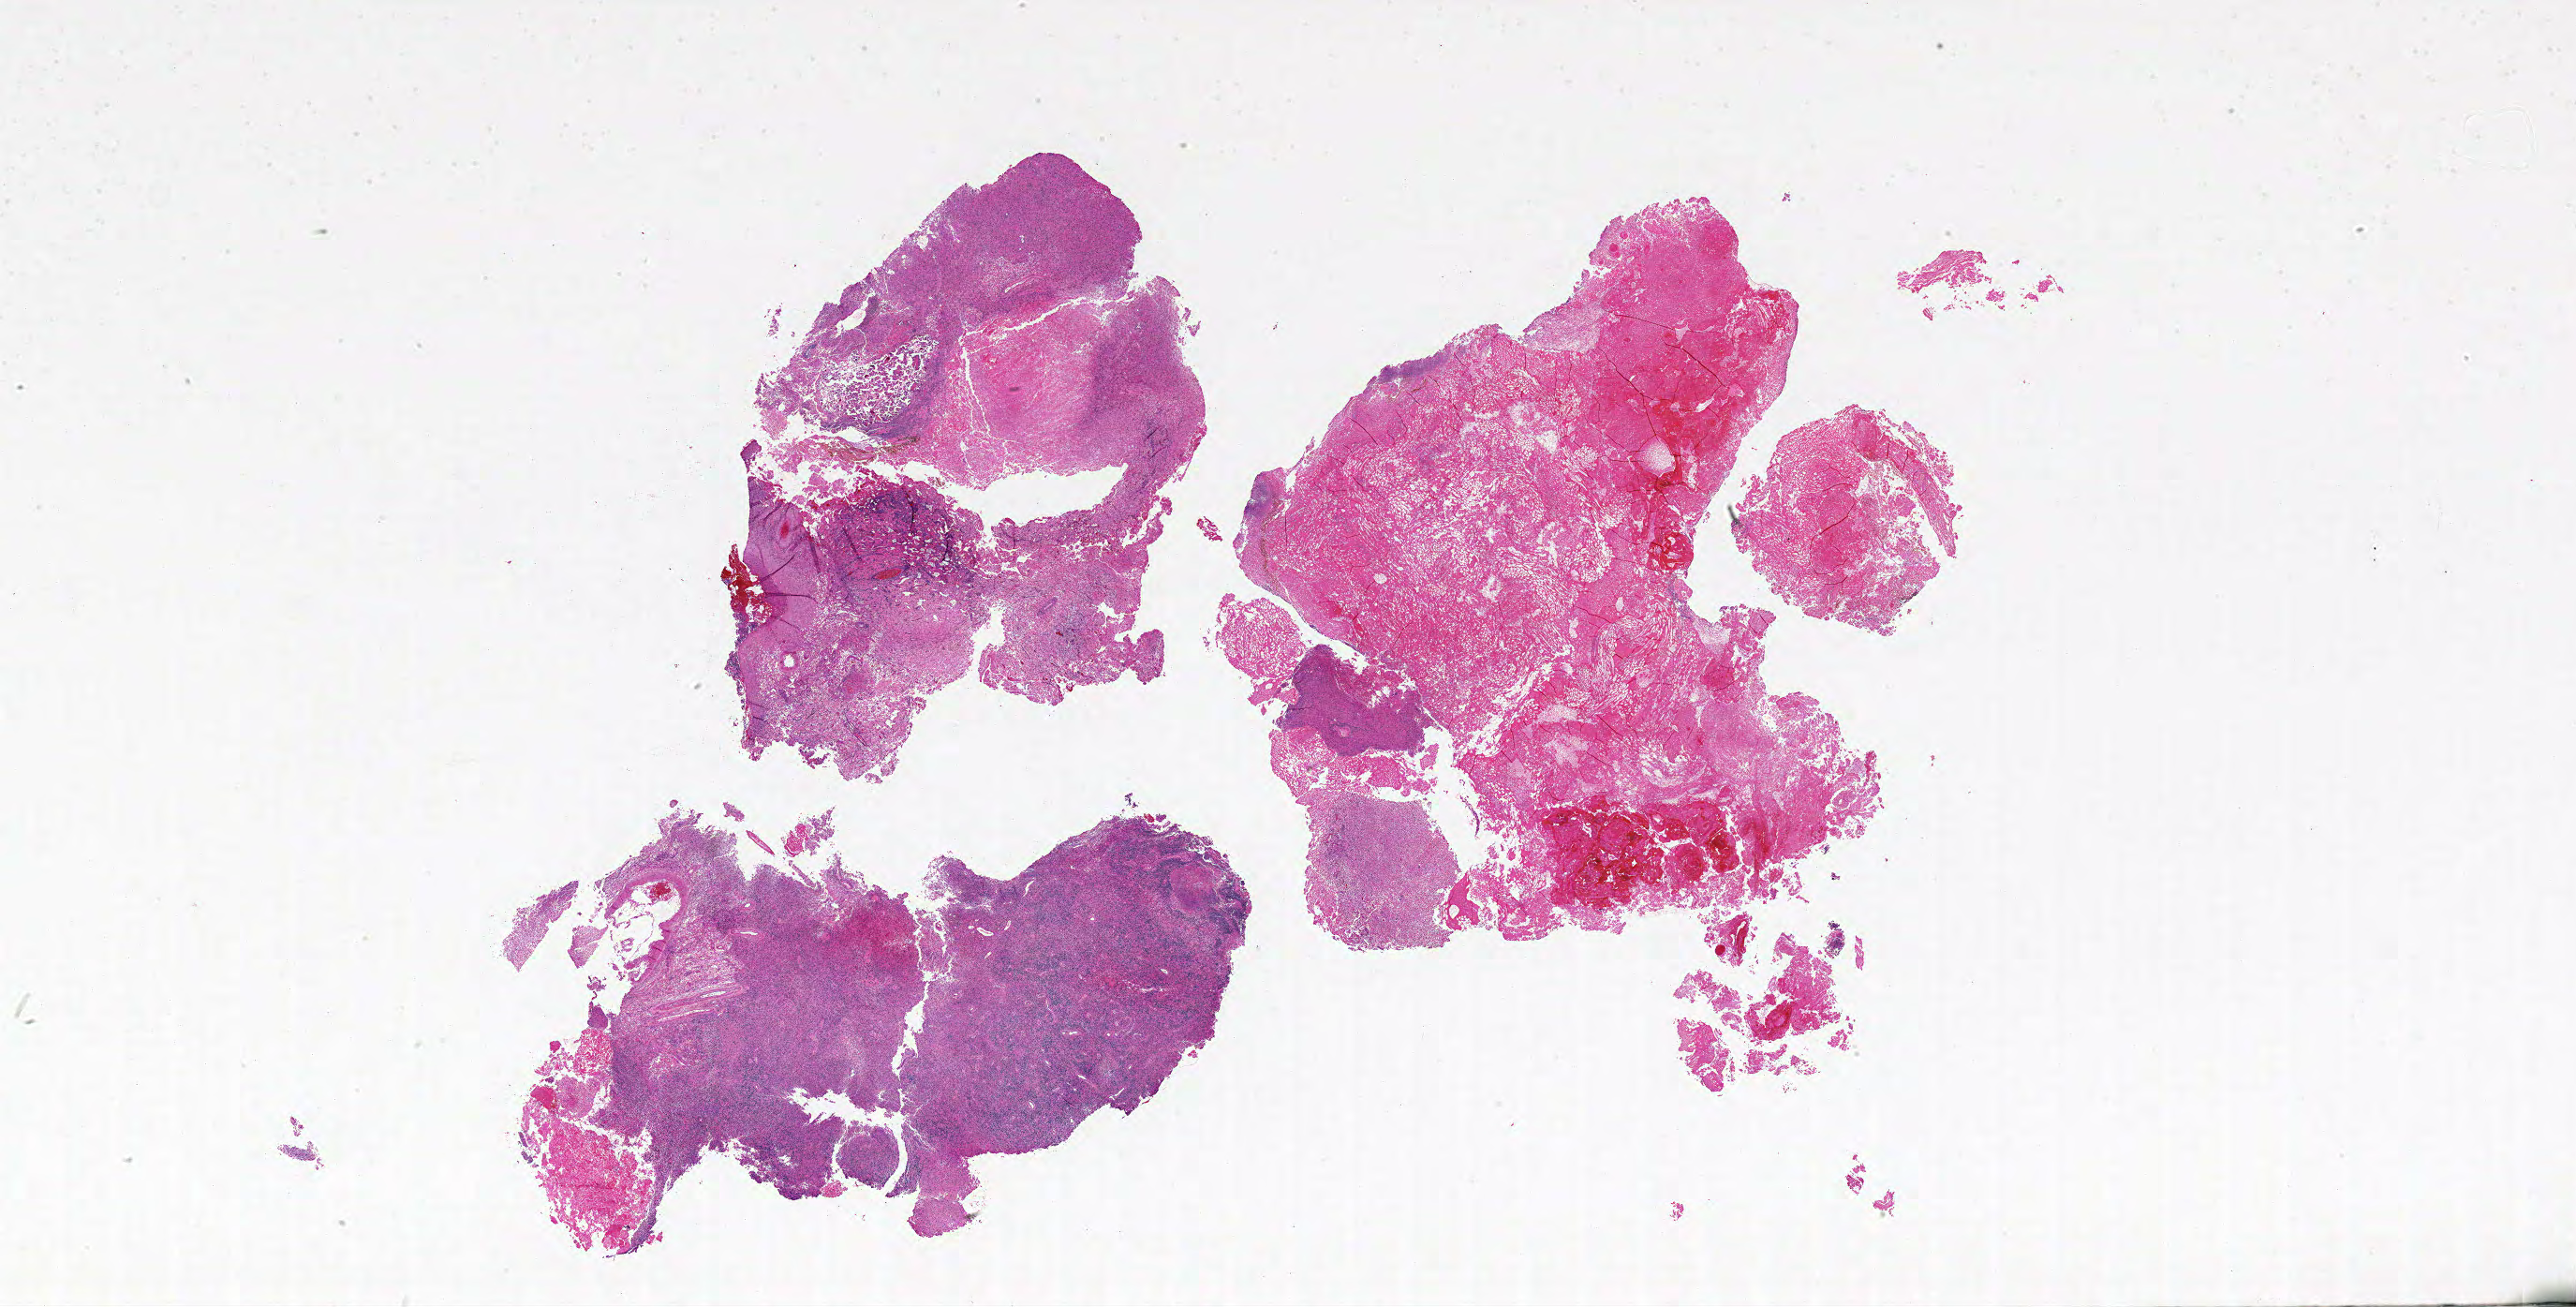
Whole-slide histology image, Hematoxylin and eosin (H&E) stained — low-resolution overview of the scanned area, about 44.0 x 22.3 mm. FFPE section. Sample: primary tumour, brain. Male patient; age at initial diagnosis 58 years.
* histologic diagnosis: Glioblastoma